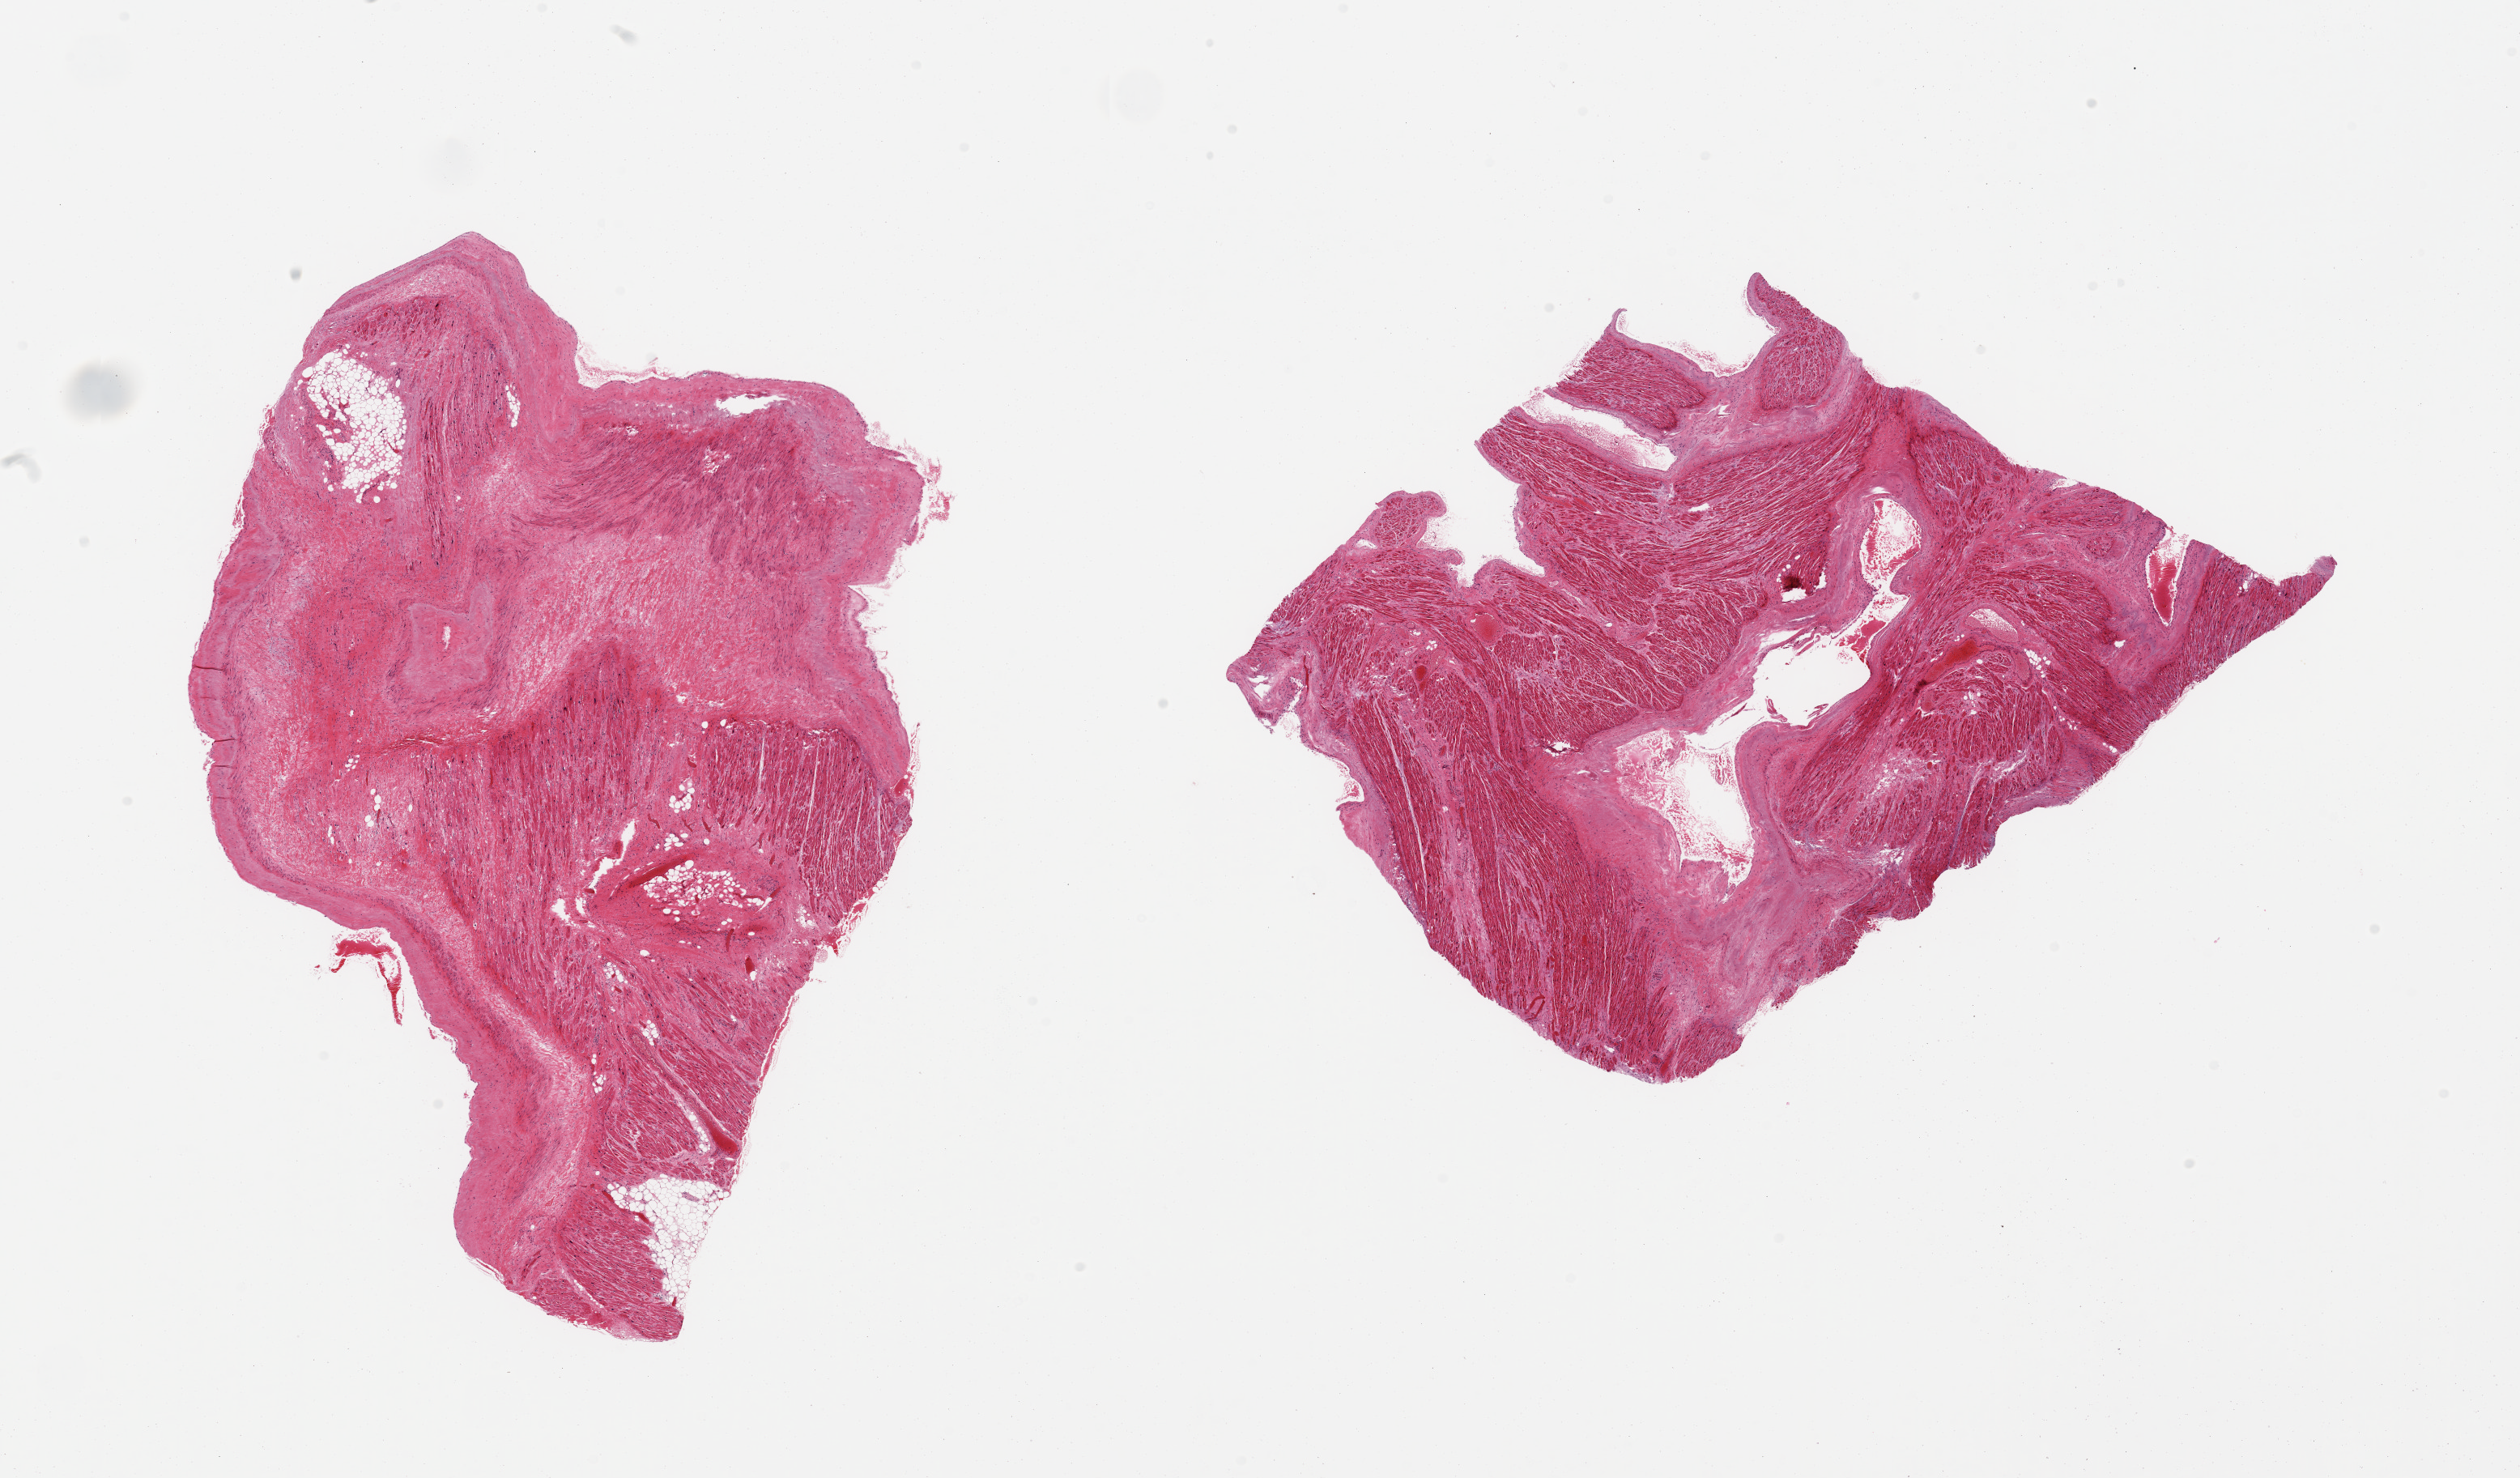
H&E whole-slide image, brightfield, a low-resolution overview of the entire scanned area, about 24.6 x 14.4 mm (from a 20x scan); PAXgene-fixed paraffin-embedded (PFPE) section; sampled site (target tissue): auricular appendage; tissue donor sample. Donor sex: female.
• pathologist's review note for this sample: 2 pieces, no abnormalities